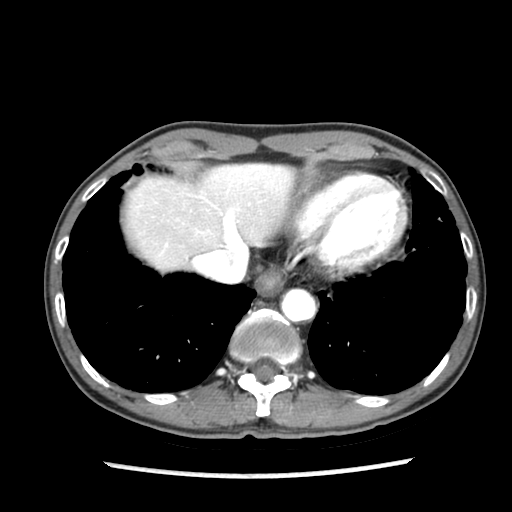
Contrast-enhanced abdominal CT (liver protocol), one axial slice. Position 72 of 87 along the scan axis. Reconstruction kernel STANDARD. 140 kVp. Soft-tissue window (W 400 / L 40 HU). 512 × 512 image matrix. Case-level facts recorded for this patient, not image findings: diagnosis: hepatocellular carcinoma (patient treated with transarterial chemoembolisation; whether this scan precedes or follows treatment is not stated here); TNM stage (as recorded): Stage-IIIB; Child-Pugh class: A; tumour differentiation: well differentiated; tumour nodularity: uninodular.
Outlined on this slice (semi-automatic segmentation, software-assisted and operator-edited):
- liver parenchyma outside the tumour (the mass and vessels are separate outlines, so this box may not span the whole liver): bounding box <124,162,314,270> (left, top, right, bottom; pixels)
- liver vessels: <166,166,272,246>